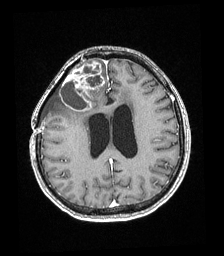
Brain MRI from a brain-tumour surgery series, one axial slice; slice 77 of 192 in the series (ordered by position); T1-weighted post-contrast; 224 × 256 image matrix, field of view 219 × 250 mm. From the clinical record (not read from this slice): histopathology: Astrocytoma; WHO grade: 4; IDH mutation: yes.
Annotated regions visible in this slice (expert manual segmentation):
- tumour: bounding box [x1, y1, x2, y2] px = [59, 61, 105, 112]